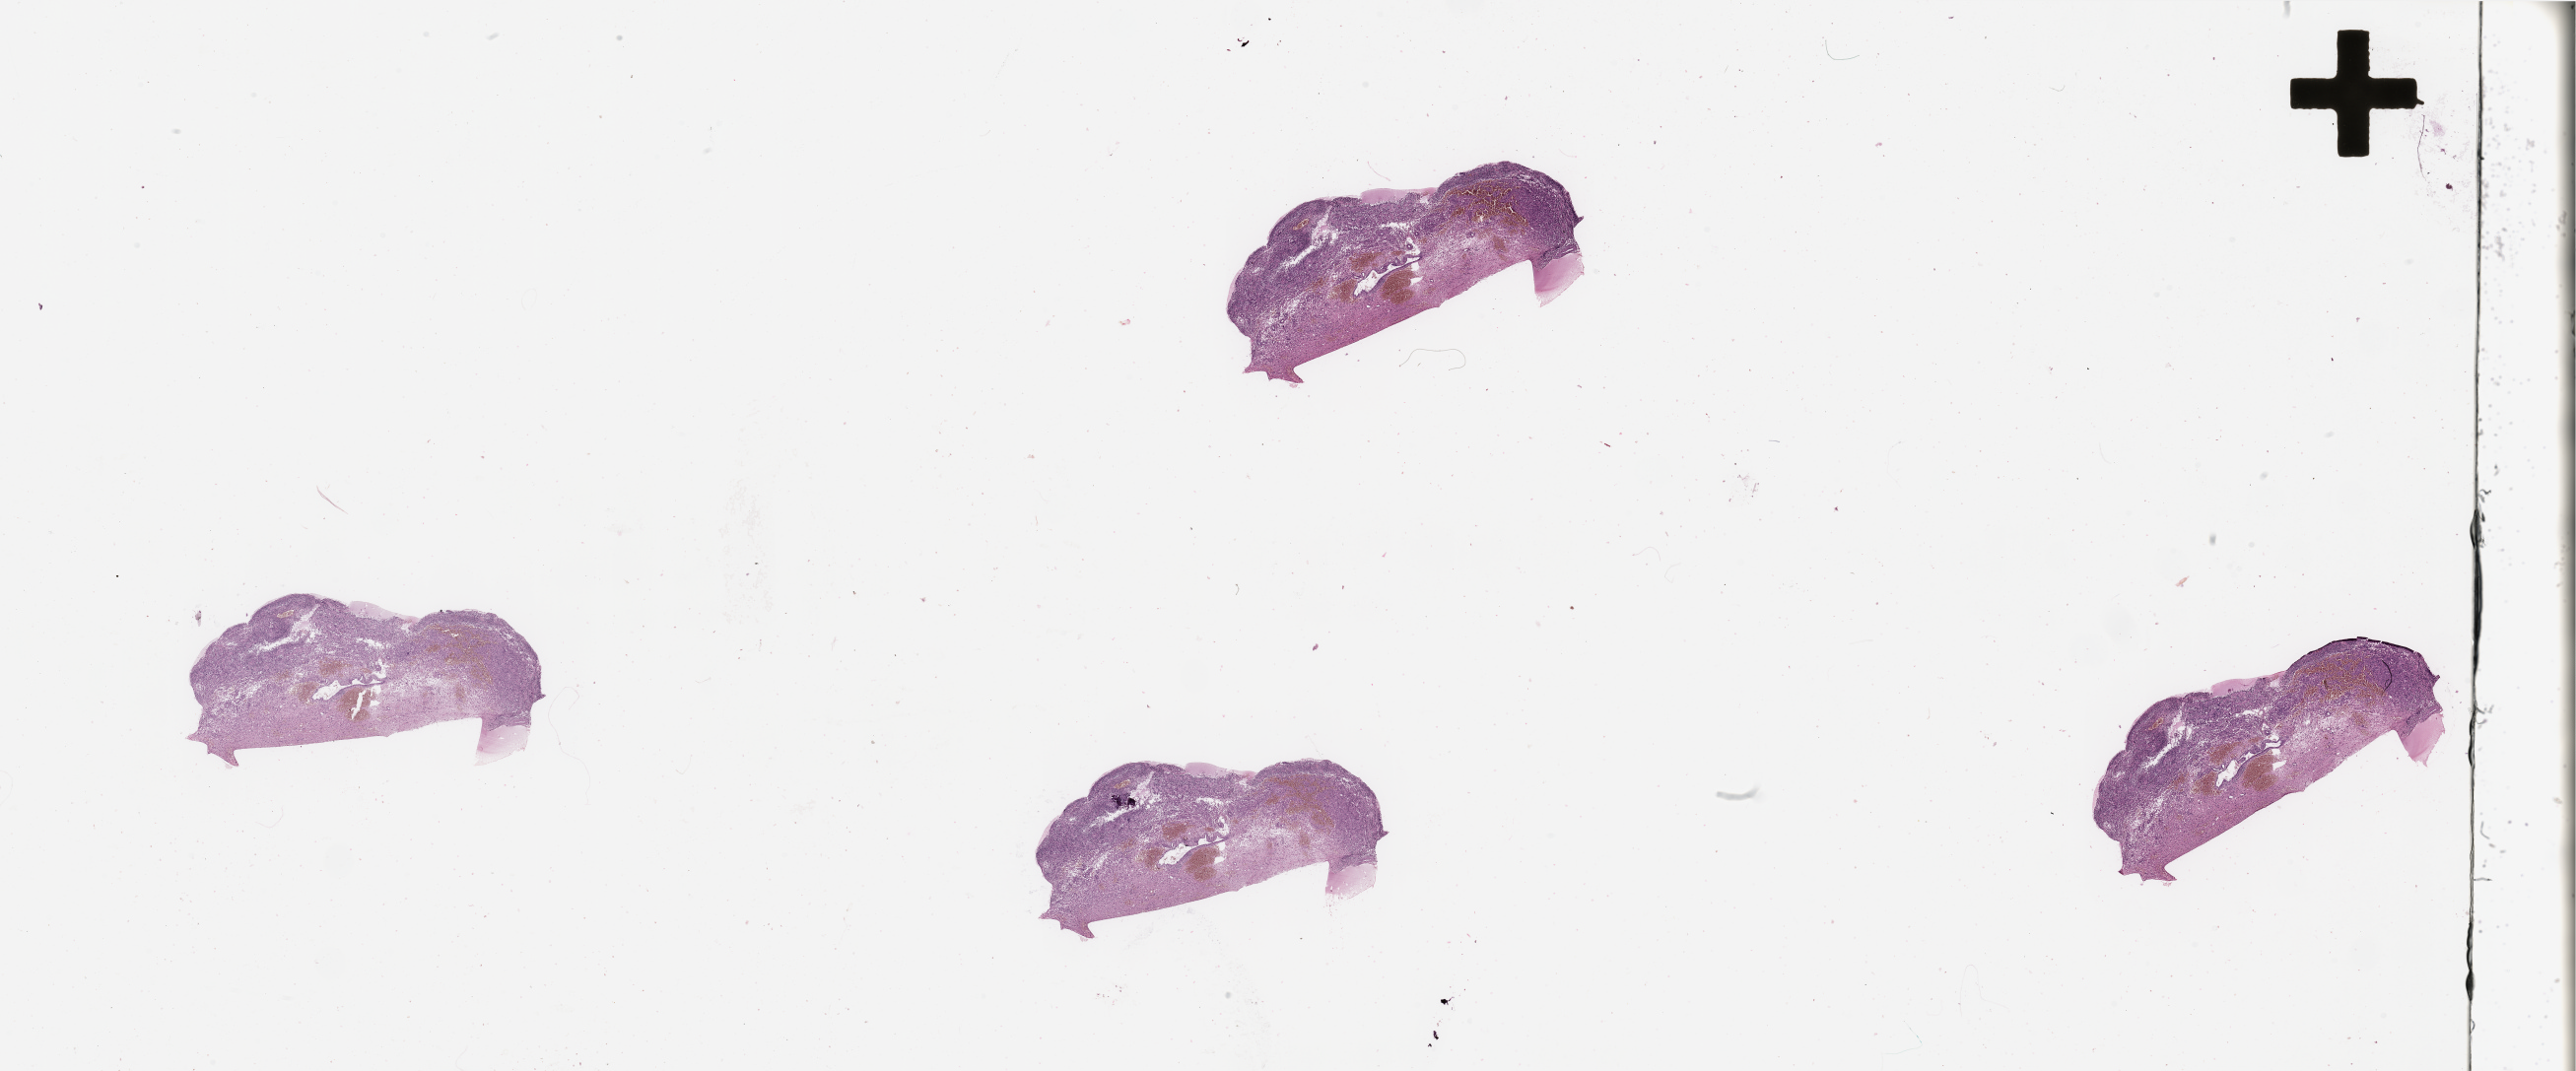
Hematoxylin and eosin (H&E) stained whole-slide image — whole scanned area (about 41.3 x 17.2 mm, from a 20x scan) shown as a low-resolution overview; tumour tissue sample, brain. Patient: female, age 58 years.
Diagnosis: Glioblastoma.